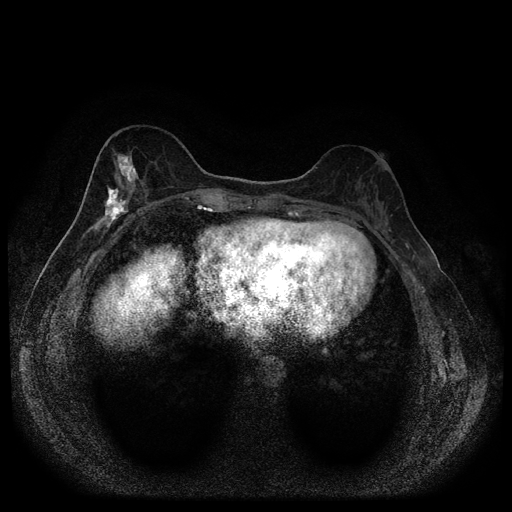
Breast MRI (dynamic contrast-enhanced, multi-phase), one axial slice; position 38 of 116 along the scan axis; dynamic contrast-enhanced series, time point 2 of 5 at this slice position (early post-contrast); 1.5 T; TE 2.7 ms, TR 5.4 ms; 2 mm slice thickness; 512 × 512 image matrix, field of view 330 × 330 mm. Female patient, age 49 years.
Annotated regions visible in this slice (semi-automatically segmented with operator editing):
- breast lesion (labelled 'tumour' in the annotation; benign lesions carry a separate 'benign' label): box from (x=83, y=150) to (x=142, y=238) px